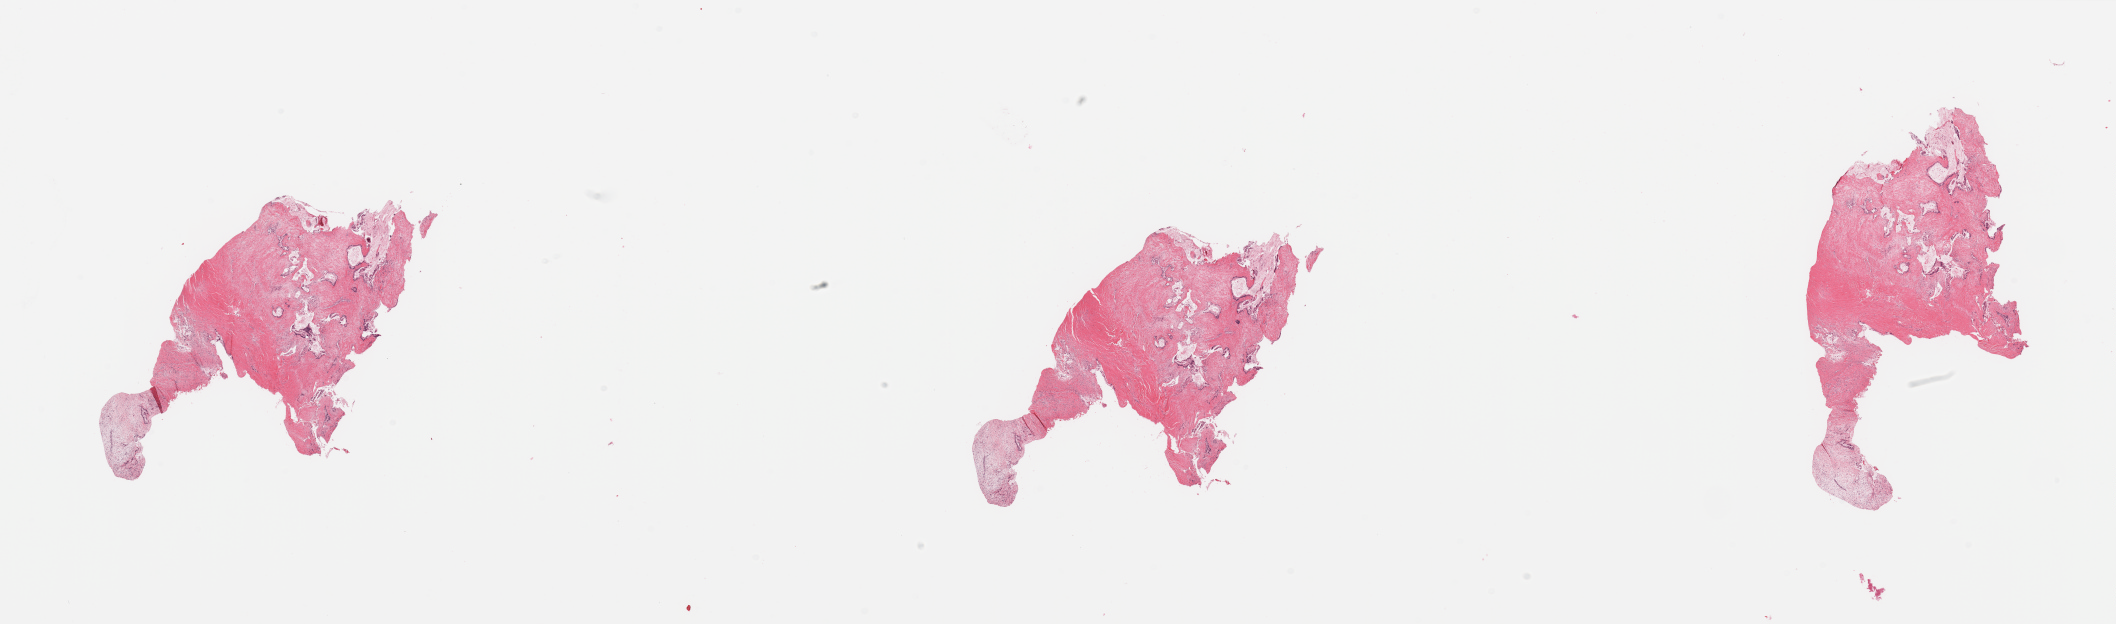
H&E whole-slide image — a low-resolution overview of the entire scanned area, about 33.5 x 9.9 mm. Tumour tissue sample, sampled site: pancreas. Patient: male, age 74 years. Composition of this section per pathologist review: tumour nuclei 10%, necrosis 2%.
Histologic diagnosis: Infiltrating duct carcinoma, NOS.